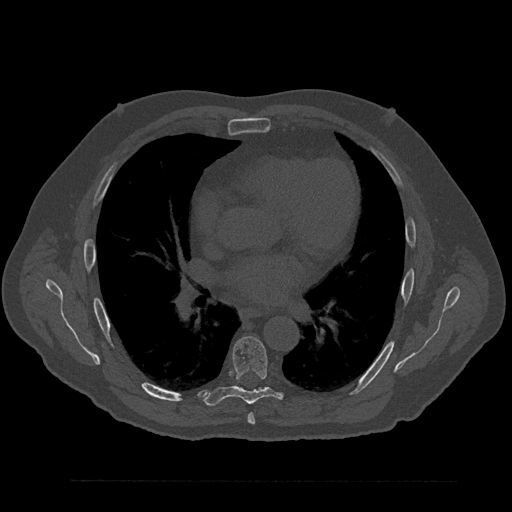
CT including the spine, one axial slice; slice 509 of 797 in the series (ordered by position); bone window (W 1800 / L 400 HU); 512 × 512 image matrix. Male patient, age 61 years. From the clinical record (not read from this slice): primary cancer: prostate.
Structures marked on this image (semi-automatic segmentation, software-assisted and operator-edited):
- T6 vertebra: bounding box [x1, y1, x2, y2] px = [248, 413, 255, 425]
- T7 vertebra: [204, 336, 282, 406]